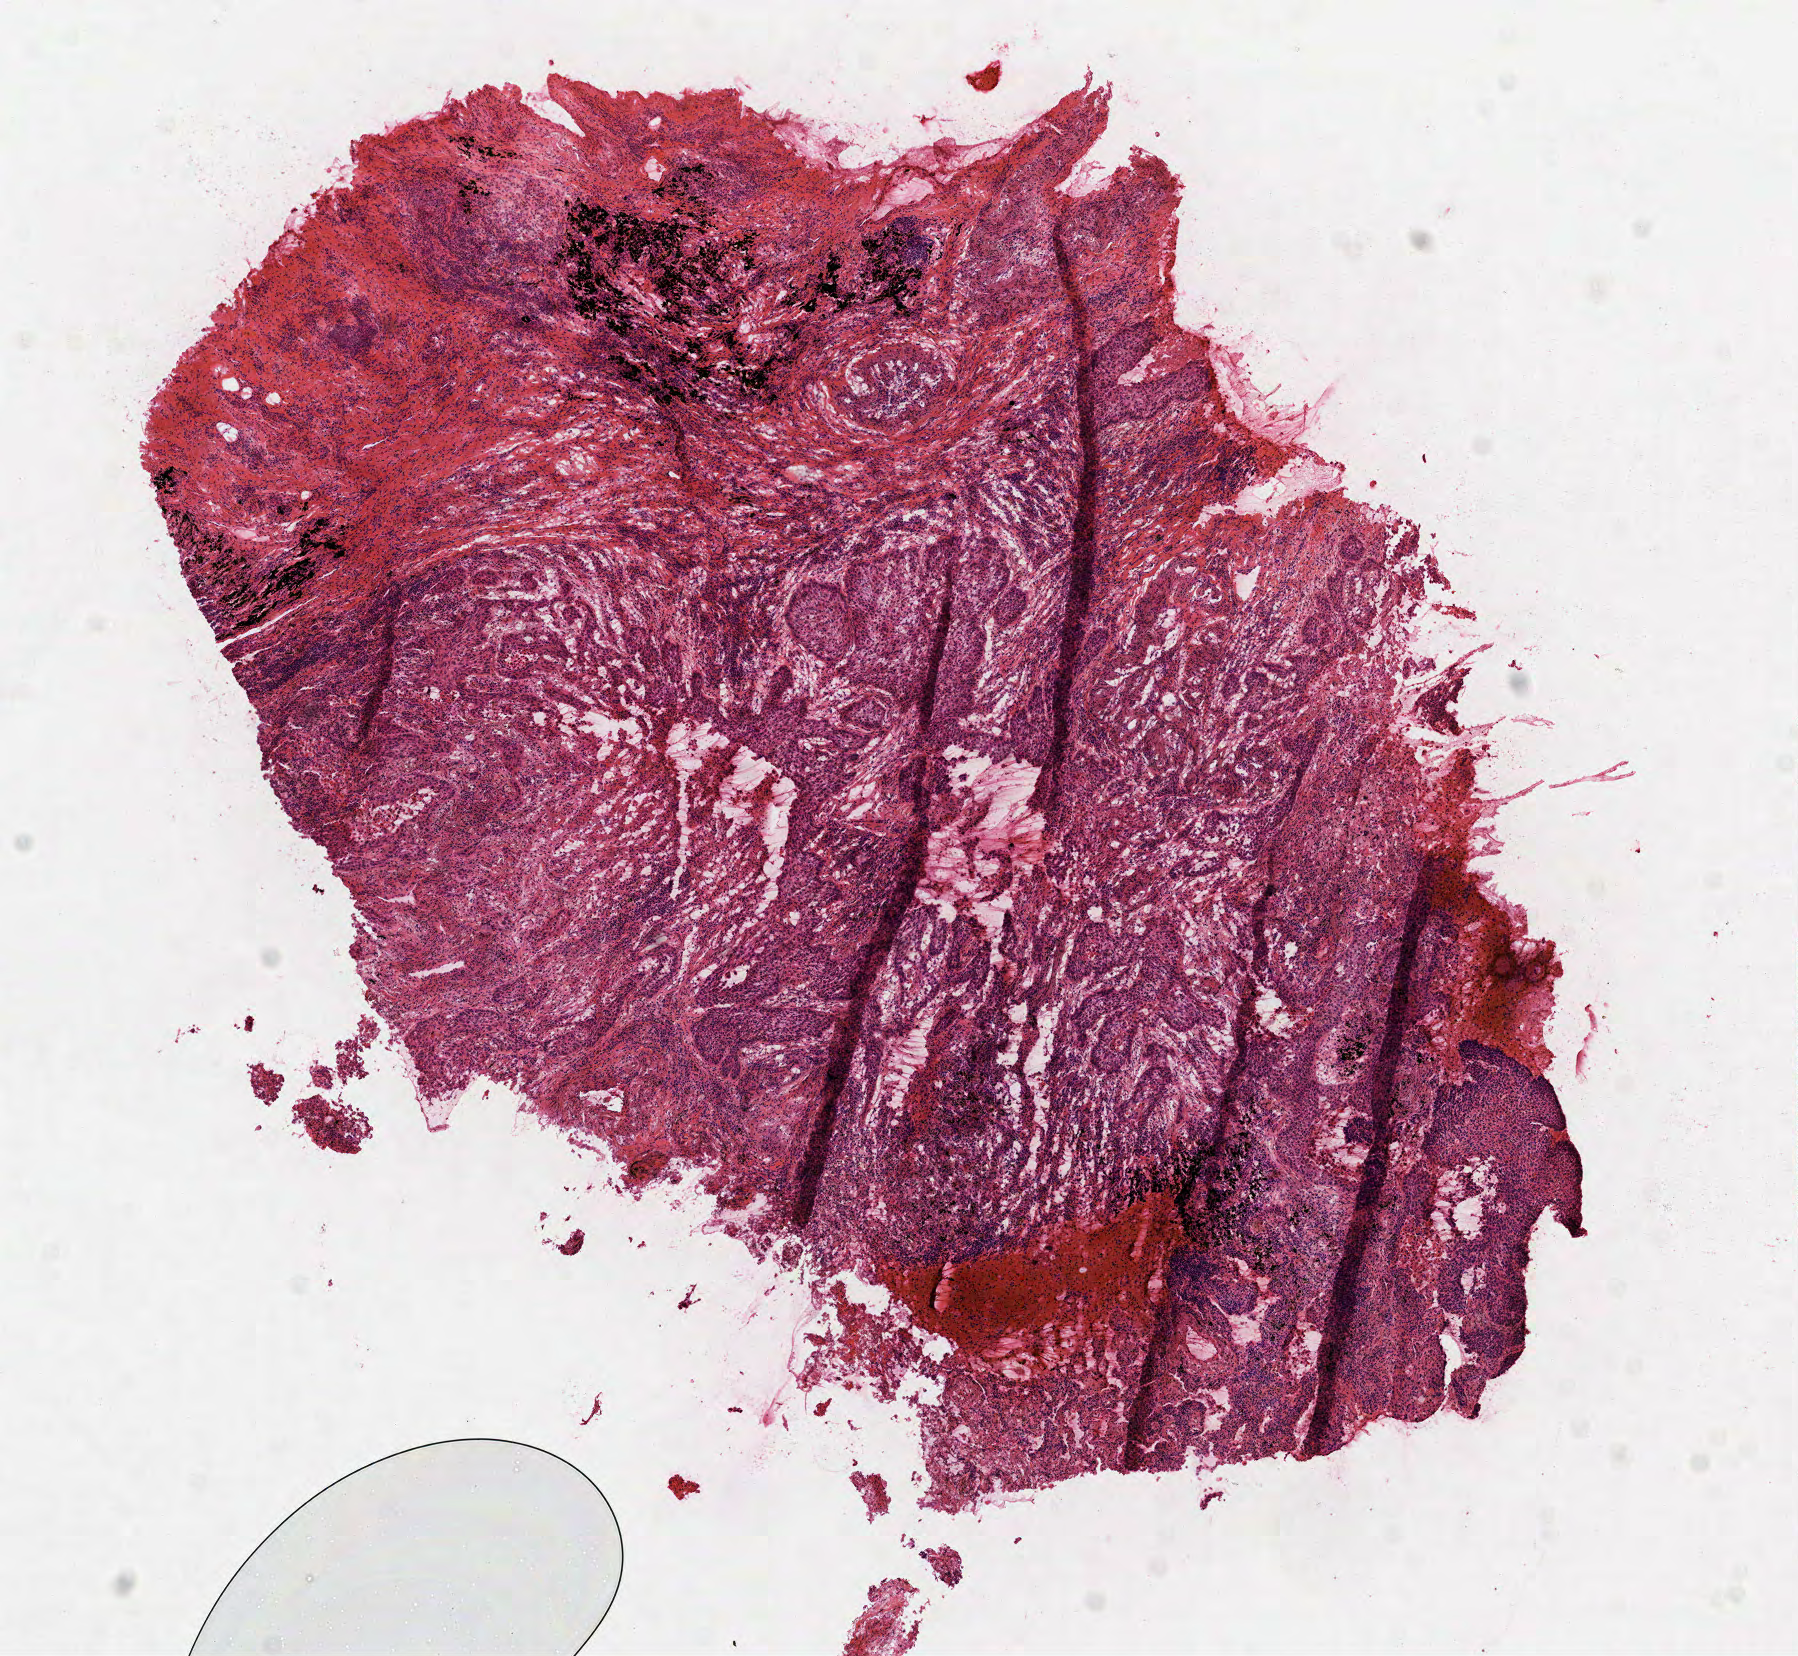
Hematoxylin and eosin (H&E) stained whole-slide image — a low-resolution overview of the entire scanned area, about 7.3 x 6.7 mm (slide scanned at 40x); formalin-fixed paraffin-embedded (FFPE) diagnostic section; lung, primary tumour sample. Male, age 64 years at initial diagnosis.
Diagnosis: Squamous cell carcinoma, NOS (upper lobe, lung). AJCC pathologic stage: IIB.